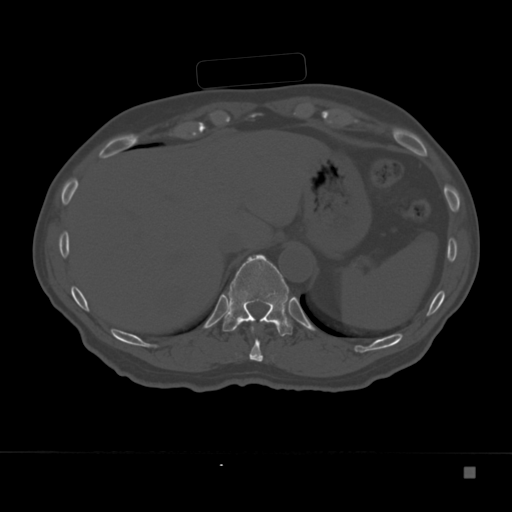
CT including the spine, one axial slice; slice 159 of 332 in the series (ordered by position); 120 kVp; bone window (W 1800 / L 400 HU); 1.5 mm slice thickness; 512 × 512 image matrix. Male patient, age 72 years. From the clinical record (not read from this slice): primary cancer: skeletal.
Outlined on this slice (semi-automatically segmented with operator editing):
- T10 vertebra: box from (x=249, y=326) to (x=278, y=362) px
- T11 vertebra: (x=223, y=254)–(x=292, y=336)